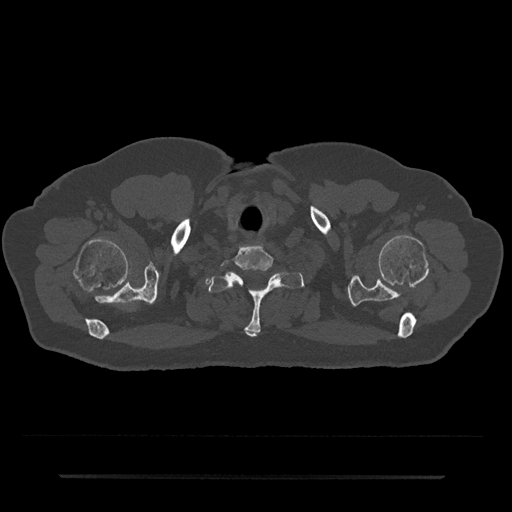
CT including the spine, one axial slice. Position 653 of 797 along the scan axis. Reconstruction kernel Br40s/3. Bone window (W 1800 / L 400 HU). 0.5 mm slice thickness. 512 × 512 image matrix, field of view 437 × 437 mm. Patient: male, 69 years. Case-level facts recorded for this patient, not image findings: primary cancer: prostate.
Outlined on this slice (semi-automatically segmented with operator editing):
- T1 vertebra: box from (x=208, y=272) to (x=304, y=337) px